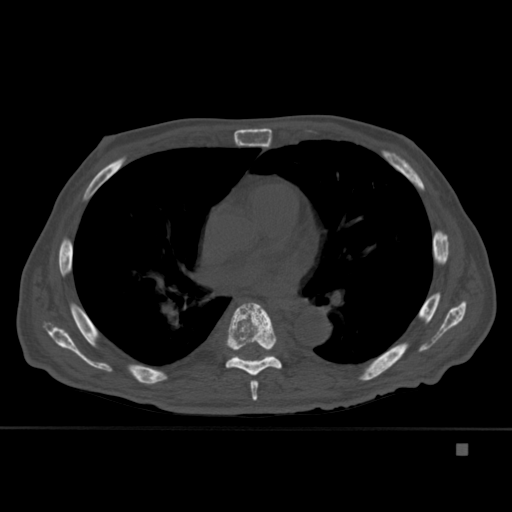
CT including the spine, one axial slice; bone window (W 1800 / L 400 HU); 1.5 mm slice thickness; 512 × 512 image matrix, field of view 378 × 378 mm. Patient: male, 75 years. From the clinical record (not read from this slice): primary cancer: prostate.
Structures marked on this image (semi-automatic segmentation, software-assisted and operator-edited):
- T4 vertebra: bounding box <270,321,274,333> (left, top, right, bottom; pixels)
- T6 vertebra: <250,380,259,401>
- T7 vertebra: <225,302,282,376>
- T8 vertebra: <228,354,275,361>